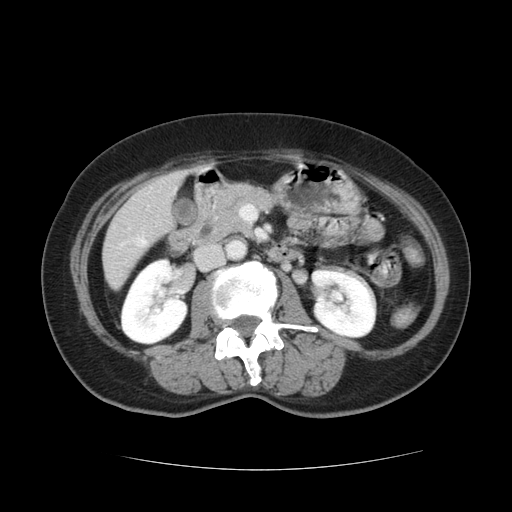
Contrast-enhanced abdominal CT, one axial slice. Position 37 of 128 along the scan axis. Soft-tissue window (W 400 / L 40 HU). 2.5 mm slice thickness. 512 × 512 image matrix. Female patient, age 67 years. Case-level facts recorded for this patient, not image findings: diagnosis: colorectal cancer liver metastases, imaged before liver resection; multiple liver metastases: yes; largest metastasis: 3 cm.
Outlined on this slice (manually delineated by an expert):
- liver: bounding box (x1, y1, x2, y2) in pixels: (104, 173, 181, 287)
- planned liver remnant (the part of the liver to remain after resection): (104, 218, 145, 287)